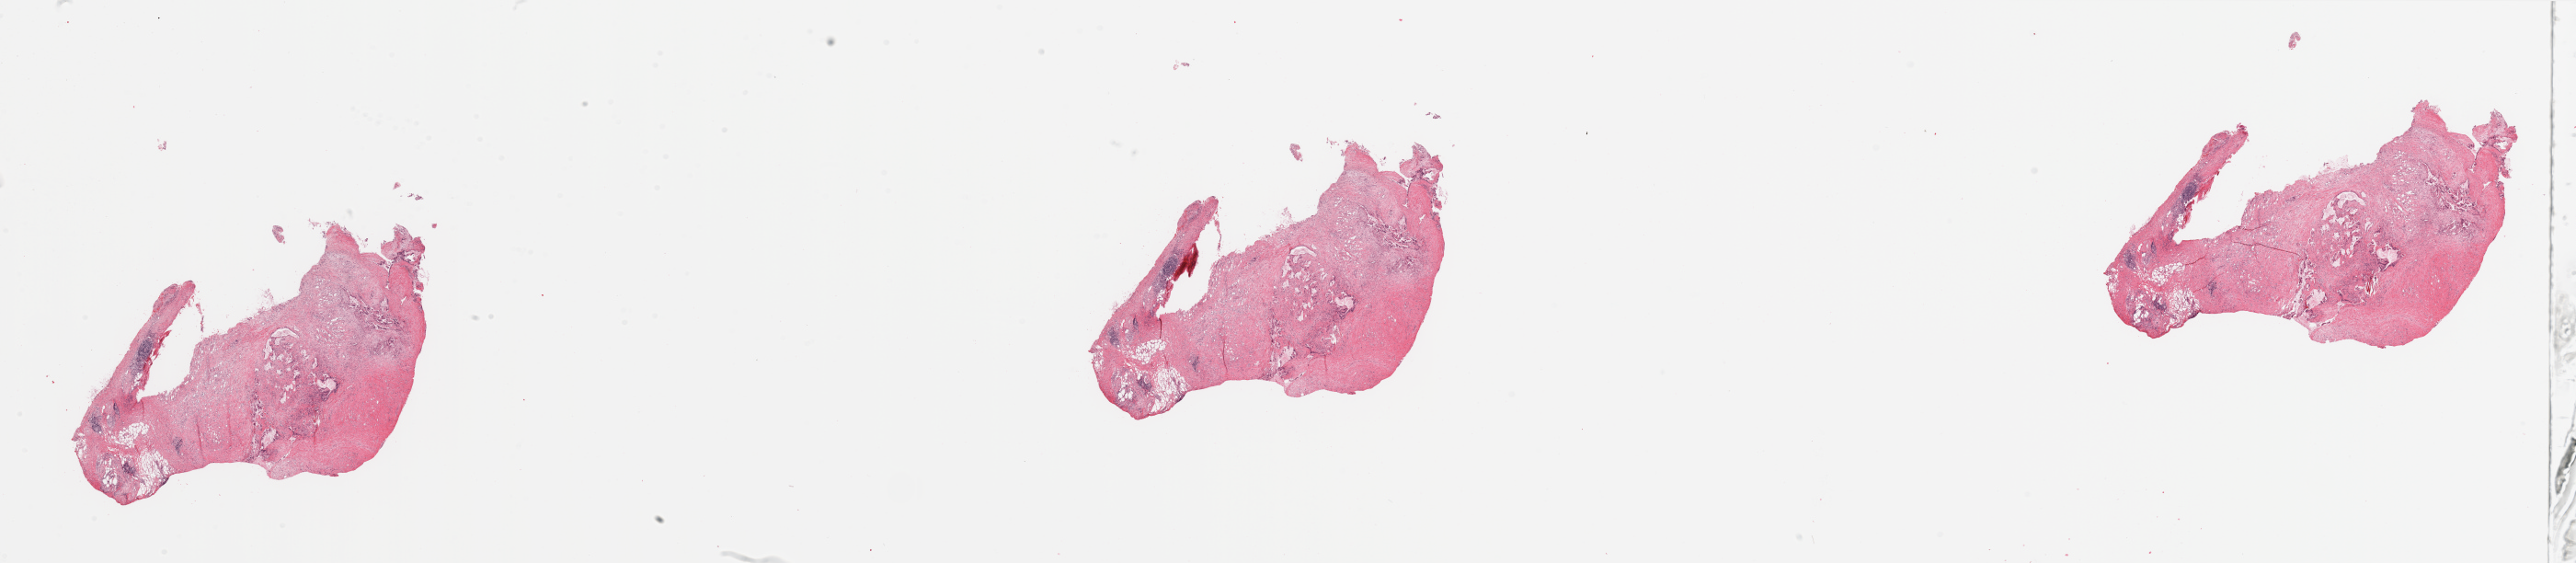
Hematoxylin and eosin (H&E) stained whole-slide image, shown as a low-resolution overview of the whole scanned area (about 44.3 x 9.7 mm, acquisition: 20x scan); pancreas, tumour tissue. Male, 74 y/o. Histologic grade: G2 (moderately differentiated).
* AJCC pathologic stage: IIA
* primary tumour site (as recorded): tail
* diagnosis: Infiltrating duct carcinoma, NOS